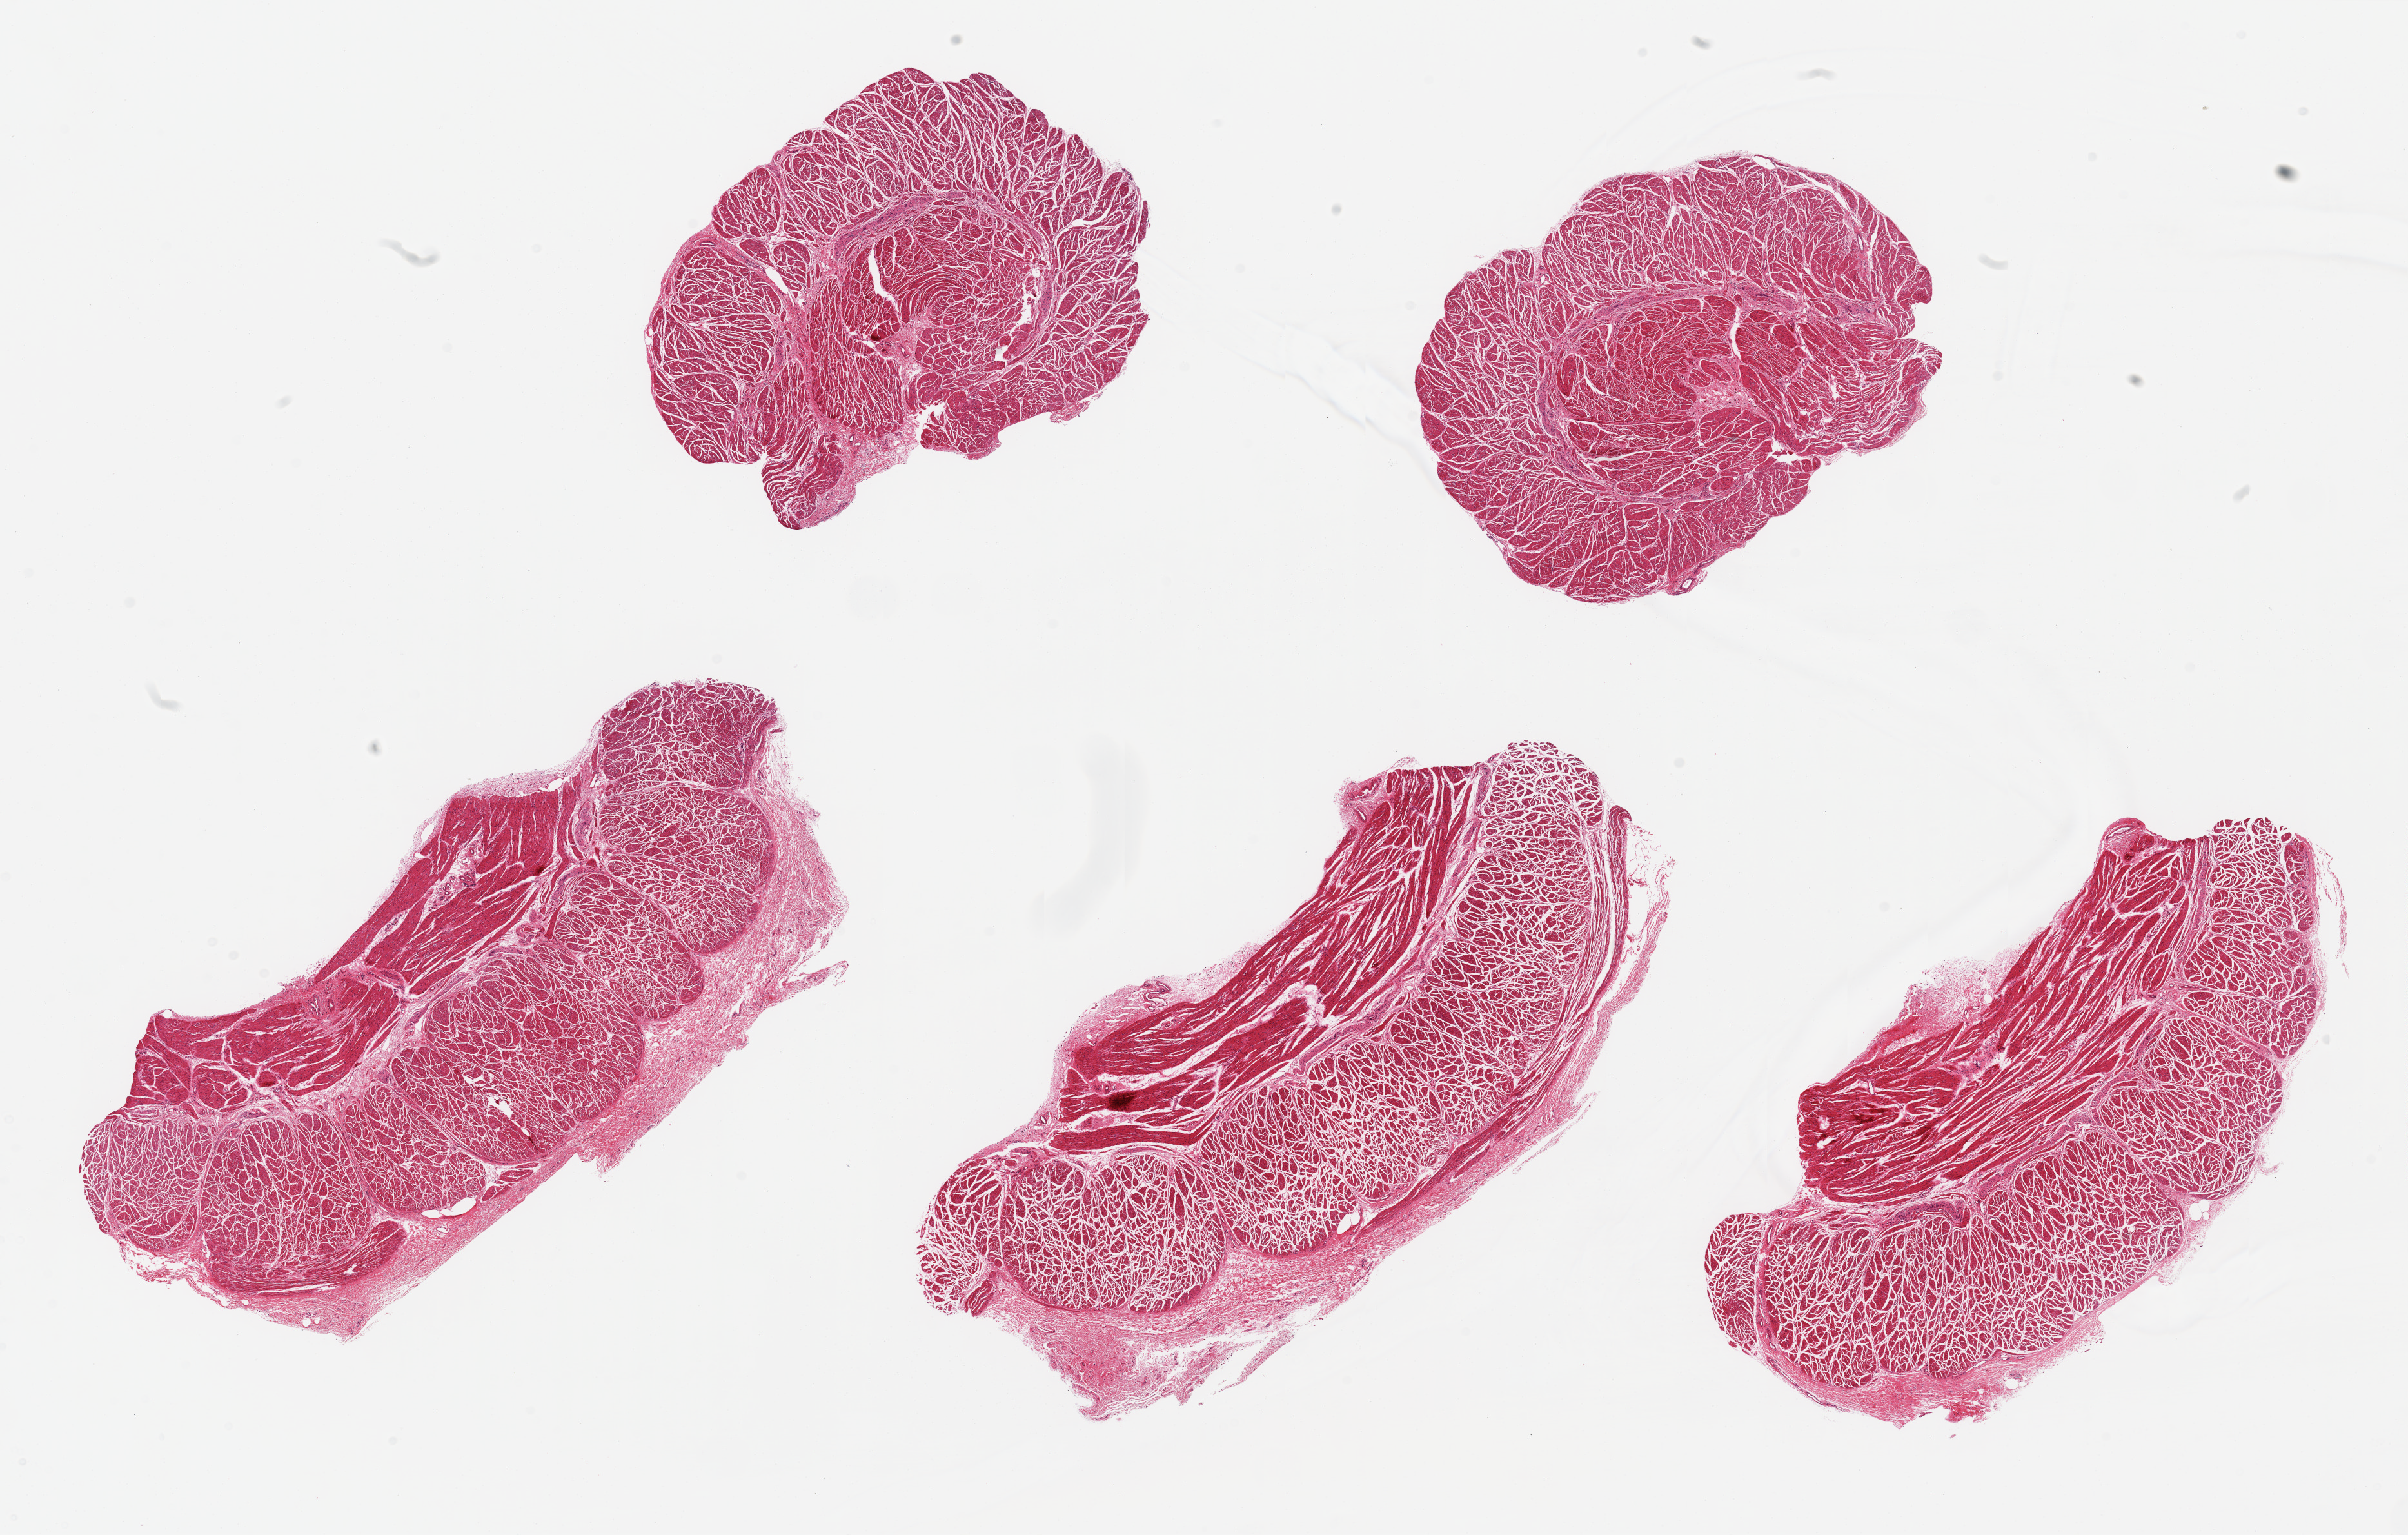
Digitized H&E-stained section, brightfield — a low-resolution overview of the entire scanned area, about 29.5 x 18.8 mm (slide scanned at 20x); PAXgene-fixed, paraffin-embedded tissue; target tissue: esophageal muscle; donor tissue sample. Donor: male.
Reviewer comment on this tissue sample: 5 pieces; well dissected.